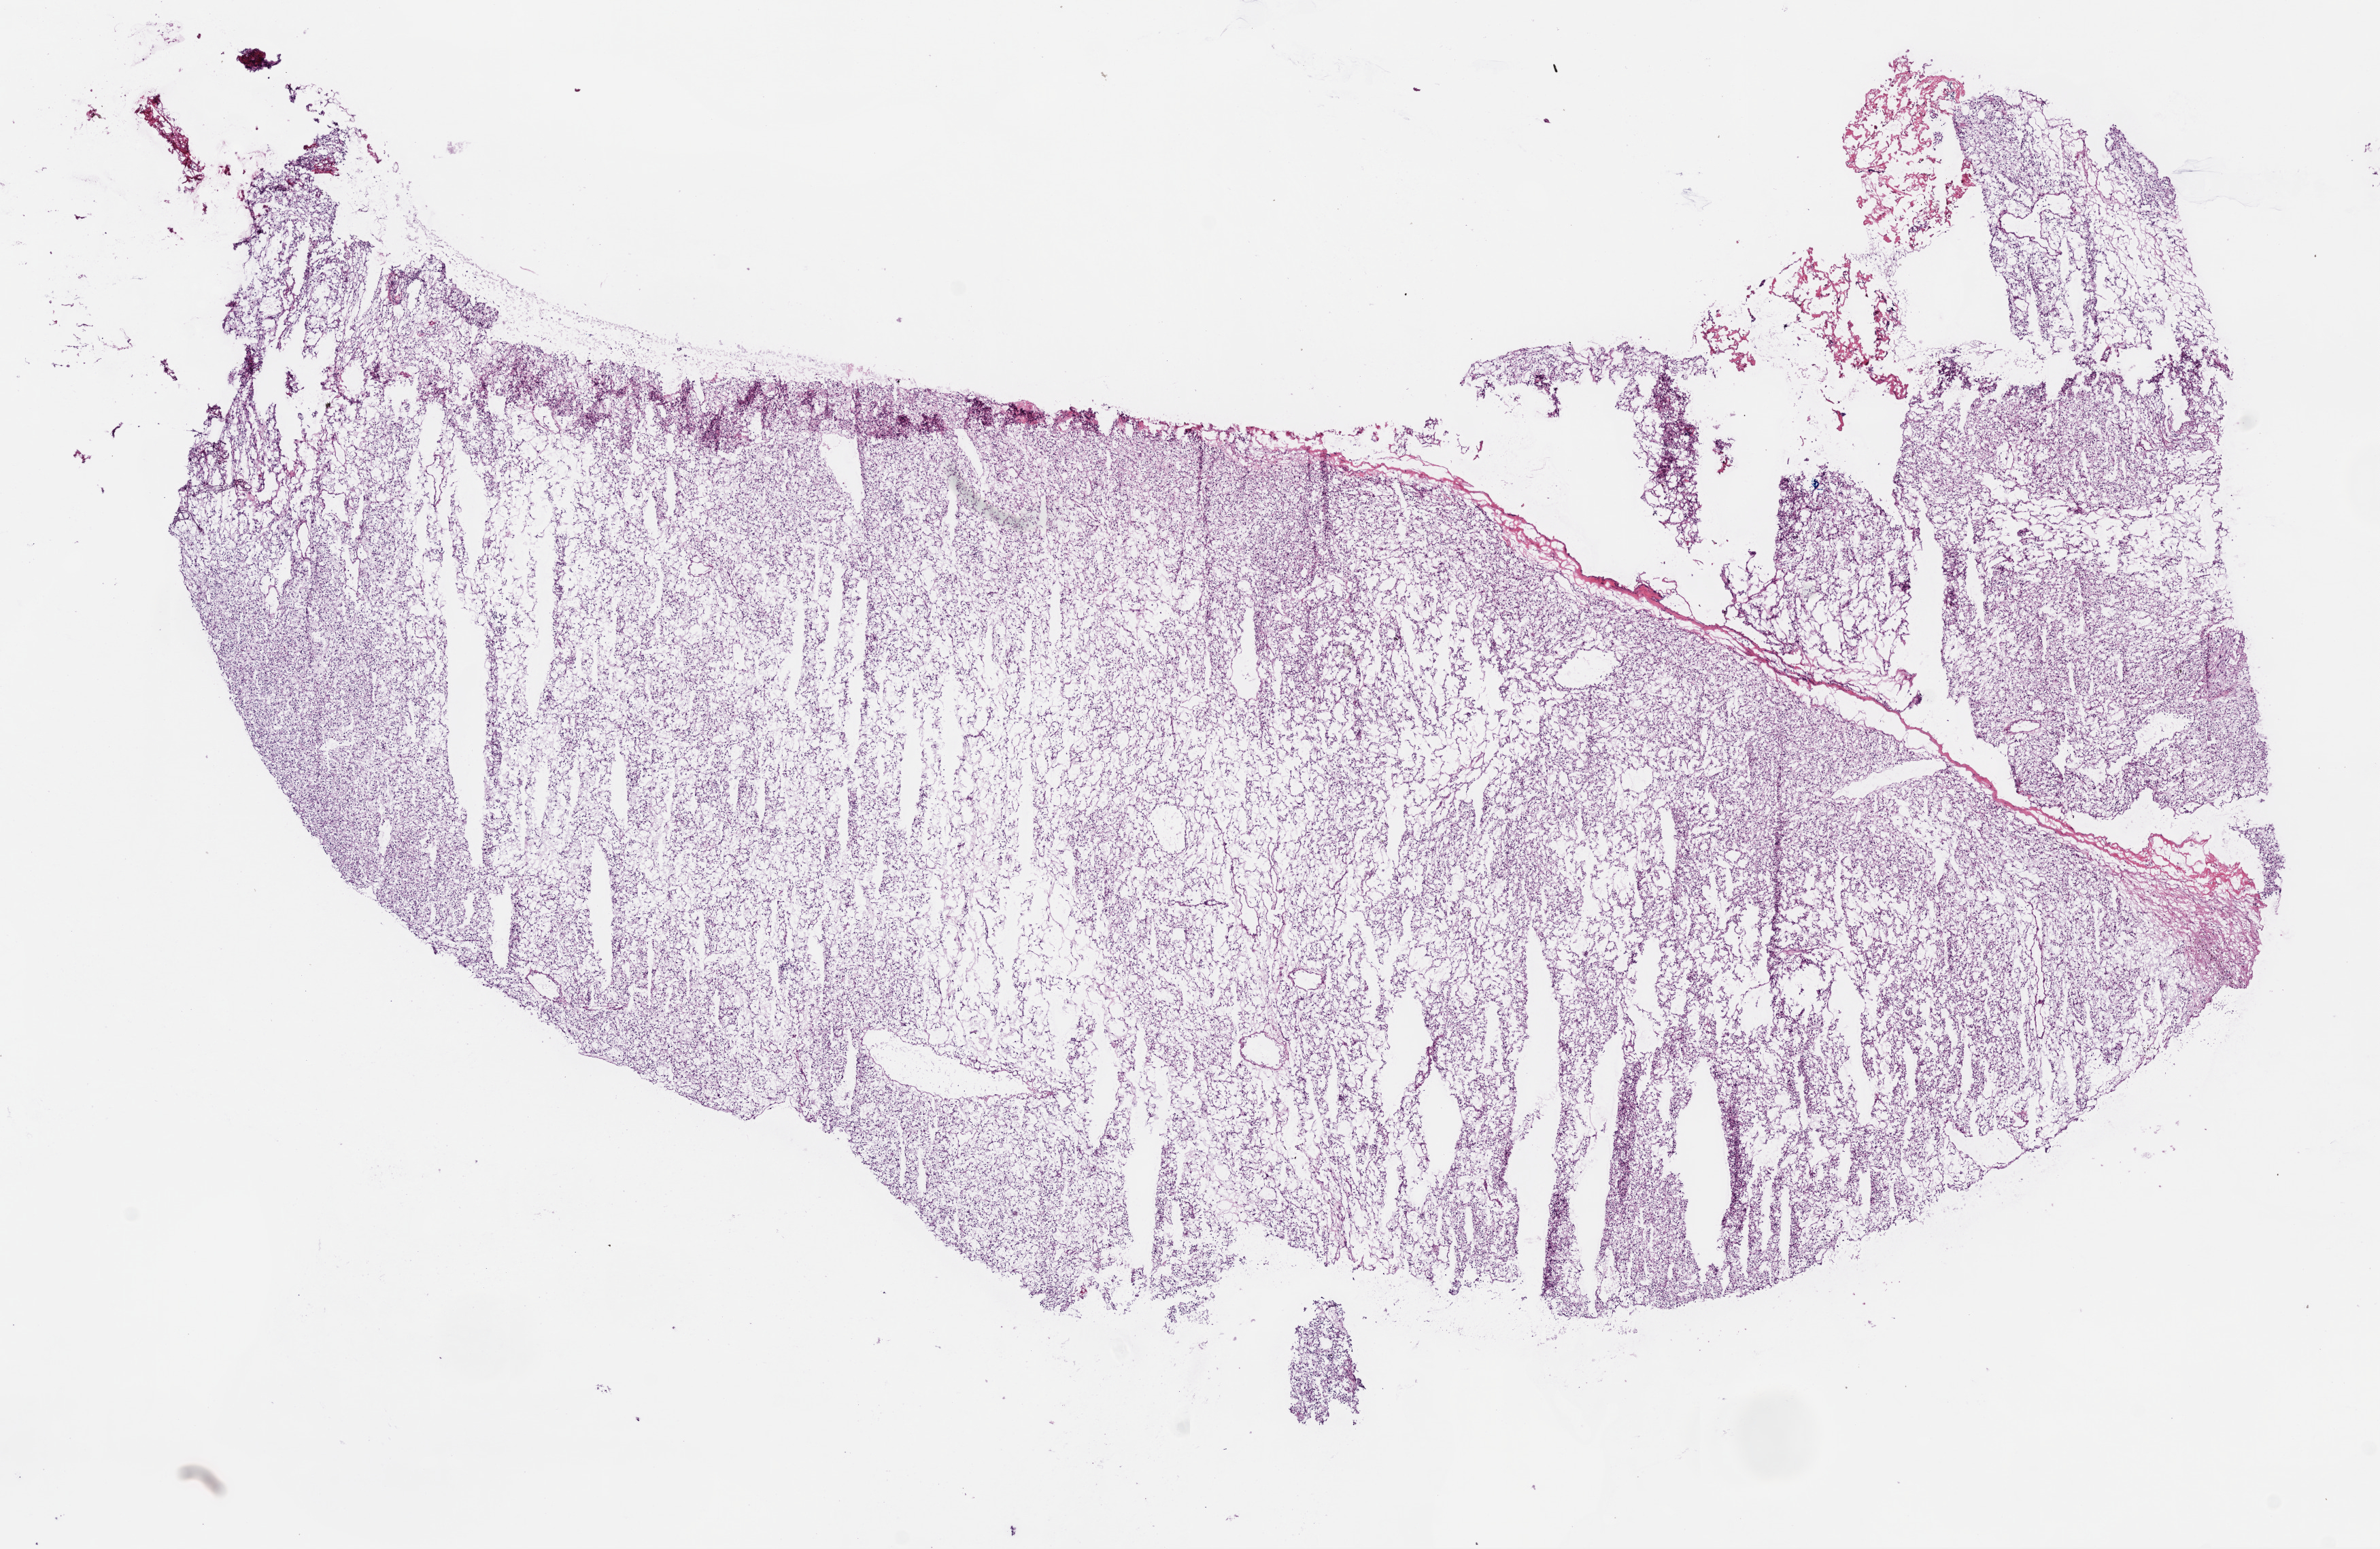
H&E-stained whole-slide image, shown as a low-resolution overview of the whole scanned area (about 14.0 x 9.1 mm, acquisition: 20x scan), frozen section from the bottom of the tissue portion, primary tumour sample from the kidney. Female, age 75 years at initial diagnosis. Histologic grade: G2 (moderately differentiated). Slide review estimates, as recorded: tumour cells 95%, tumour nuclei 85%, normal cells 0%, stromal cells 5%, necrosis 0%.
• pathologic diagnosis: Clear cell adenocarcinoma, NOS
• AJCC pathologic stage: I